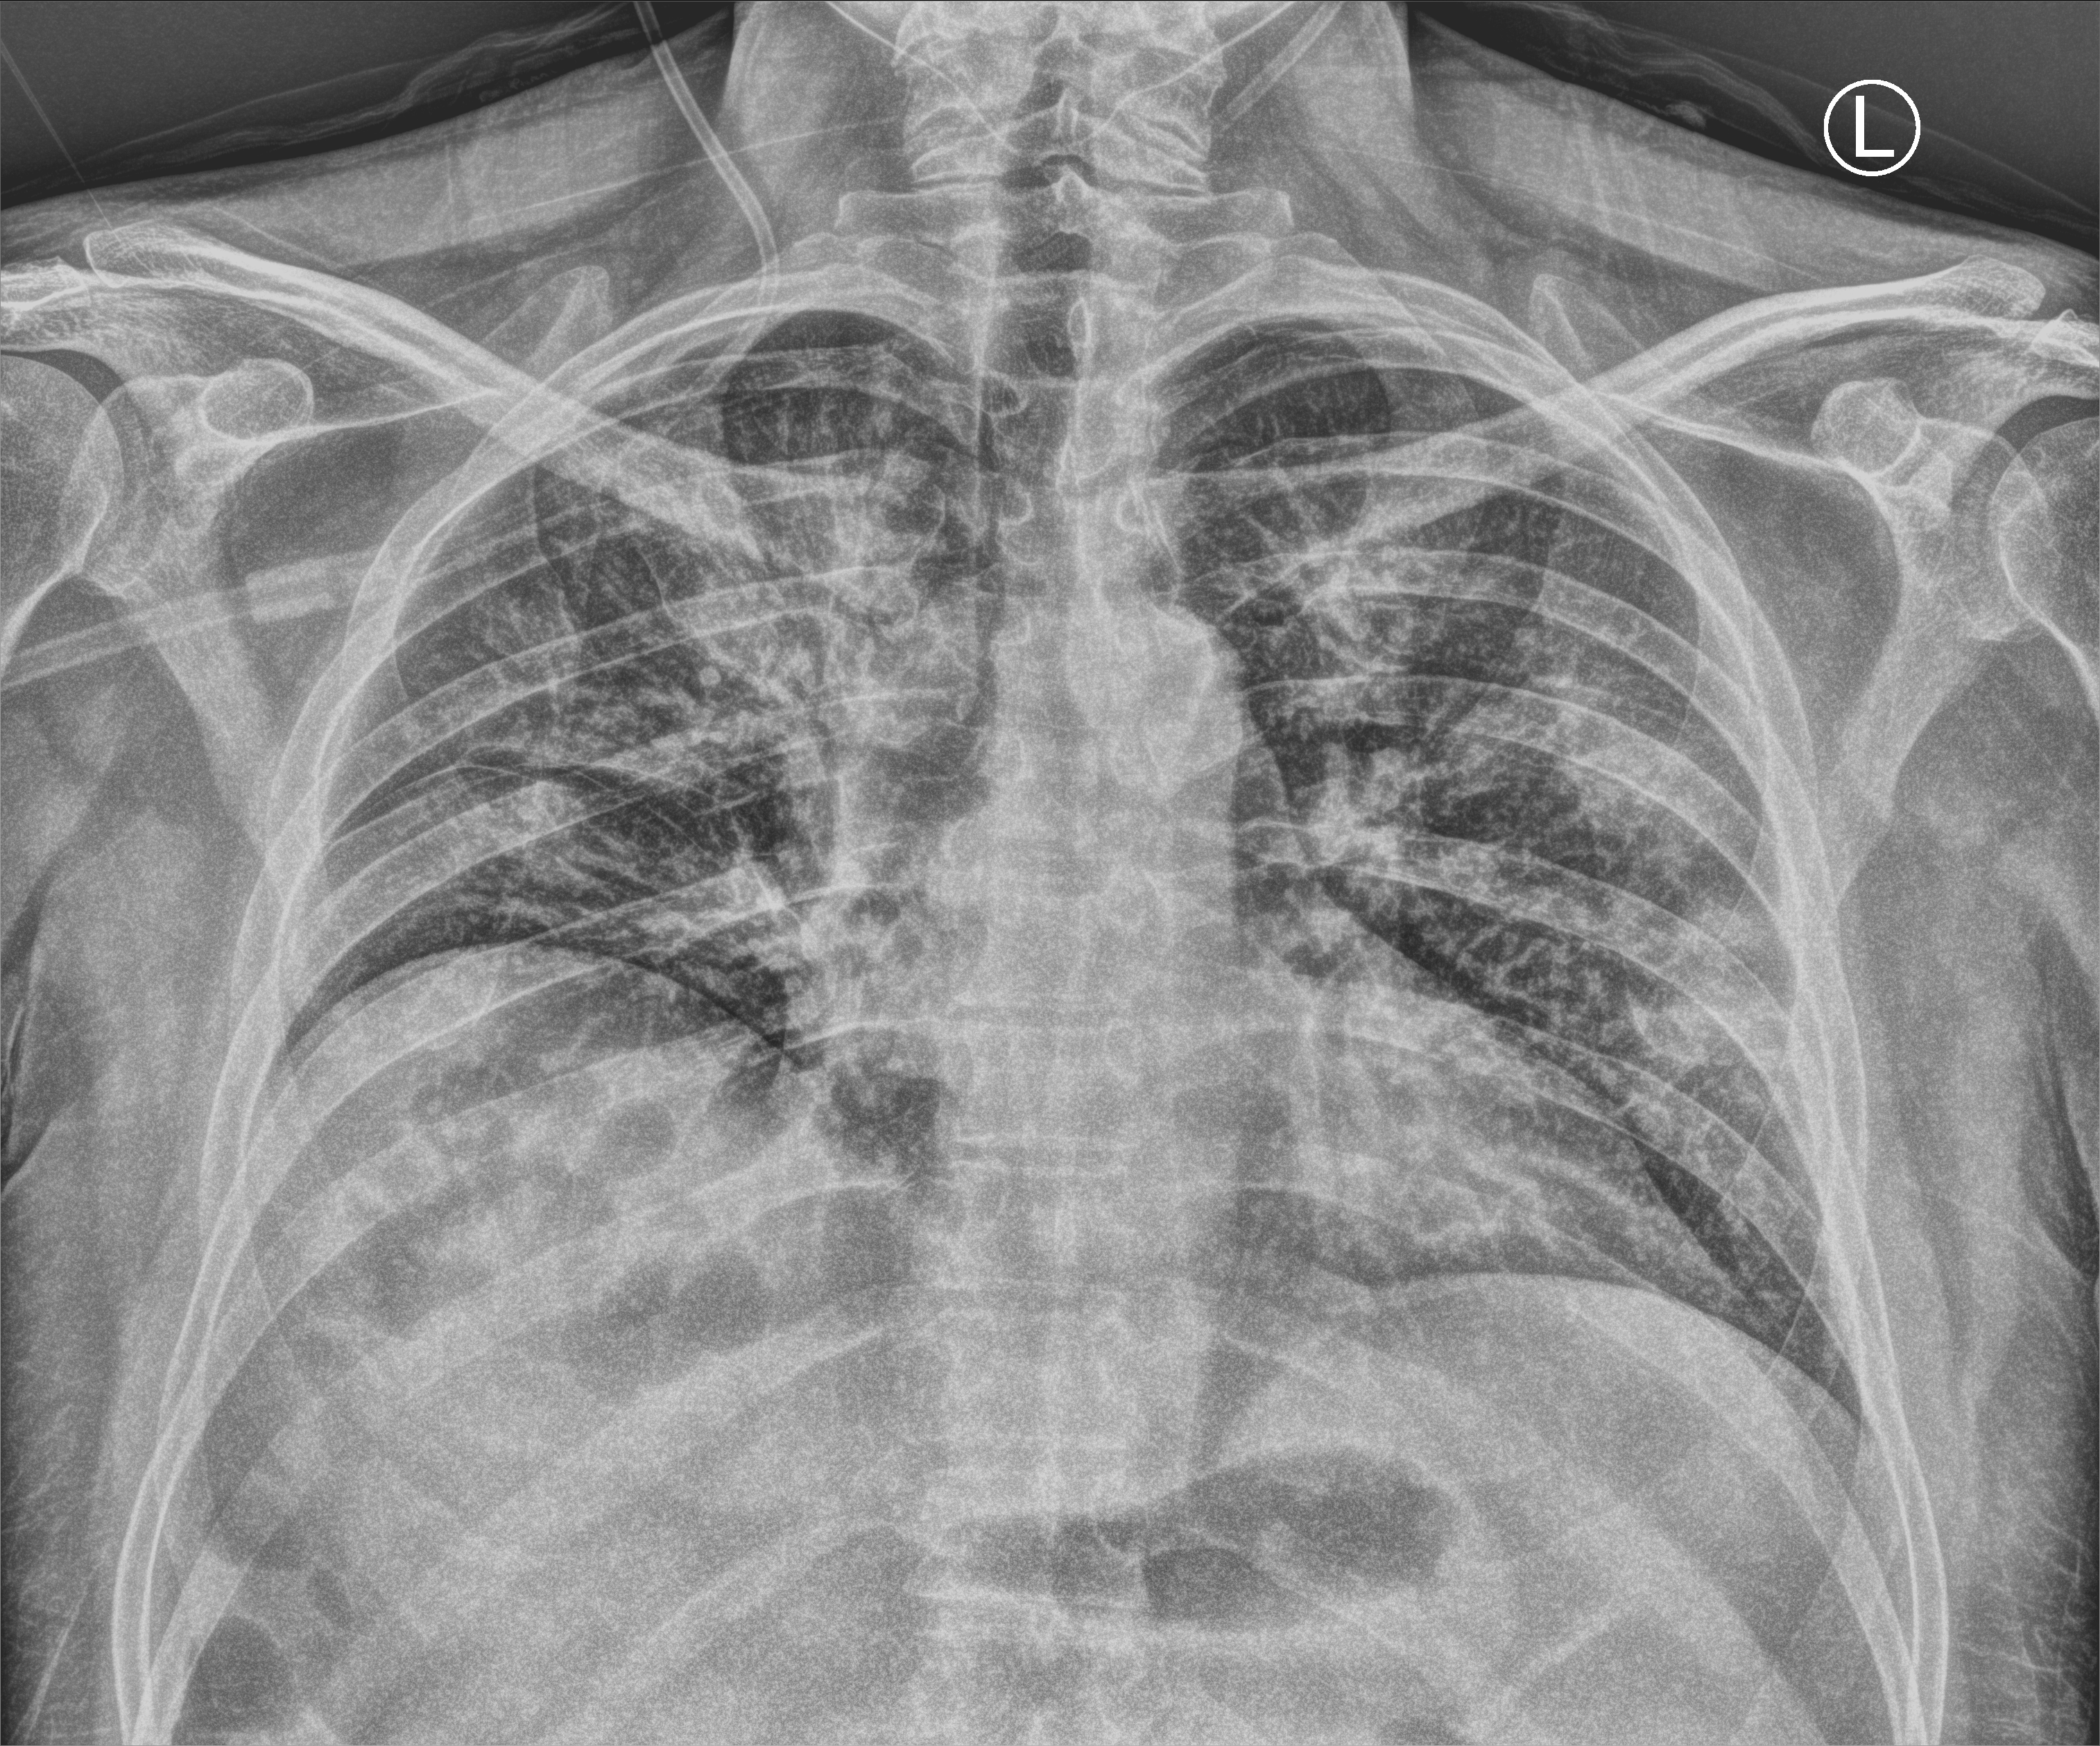
Chest X-ray (portable). Male patient hospitalised with COVID-19, age 18–59 years.
Admission-level facts for this patient (not findings on this image; timing relative to this image not recorded): diabetes (admission record): no; mechanically ventilated during this hospital stay: yes.